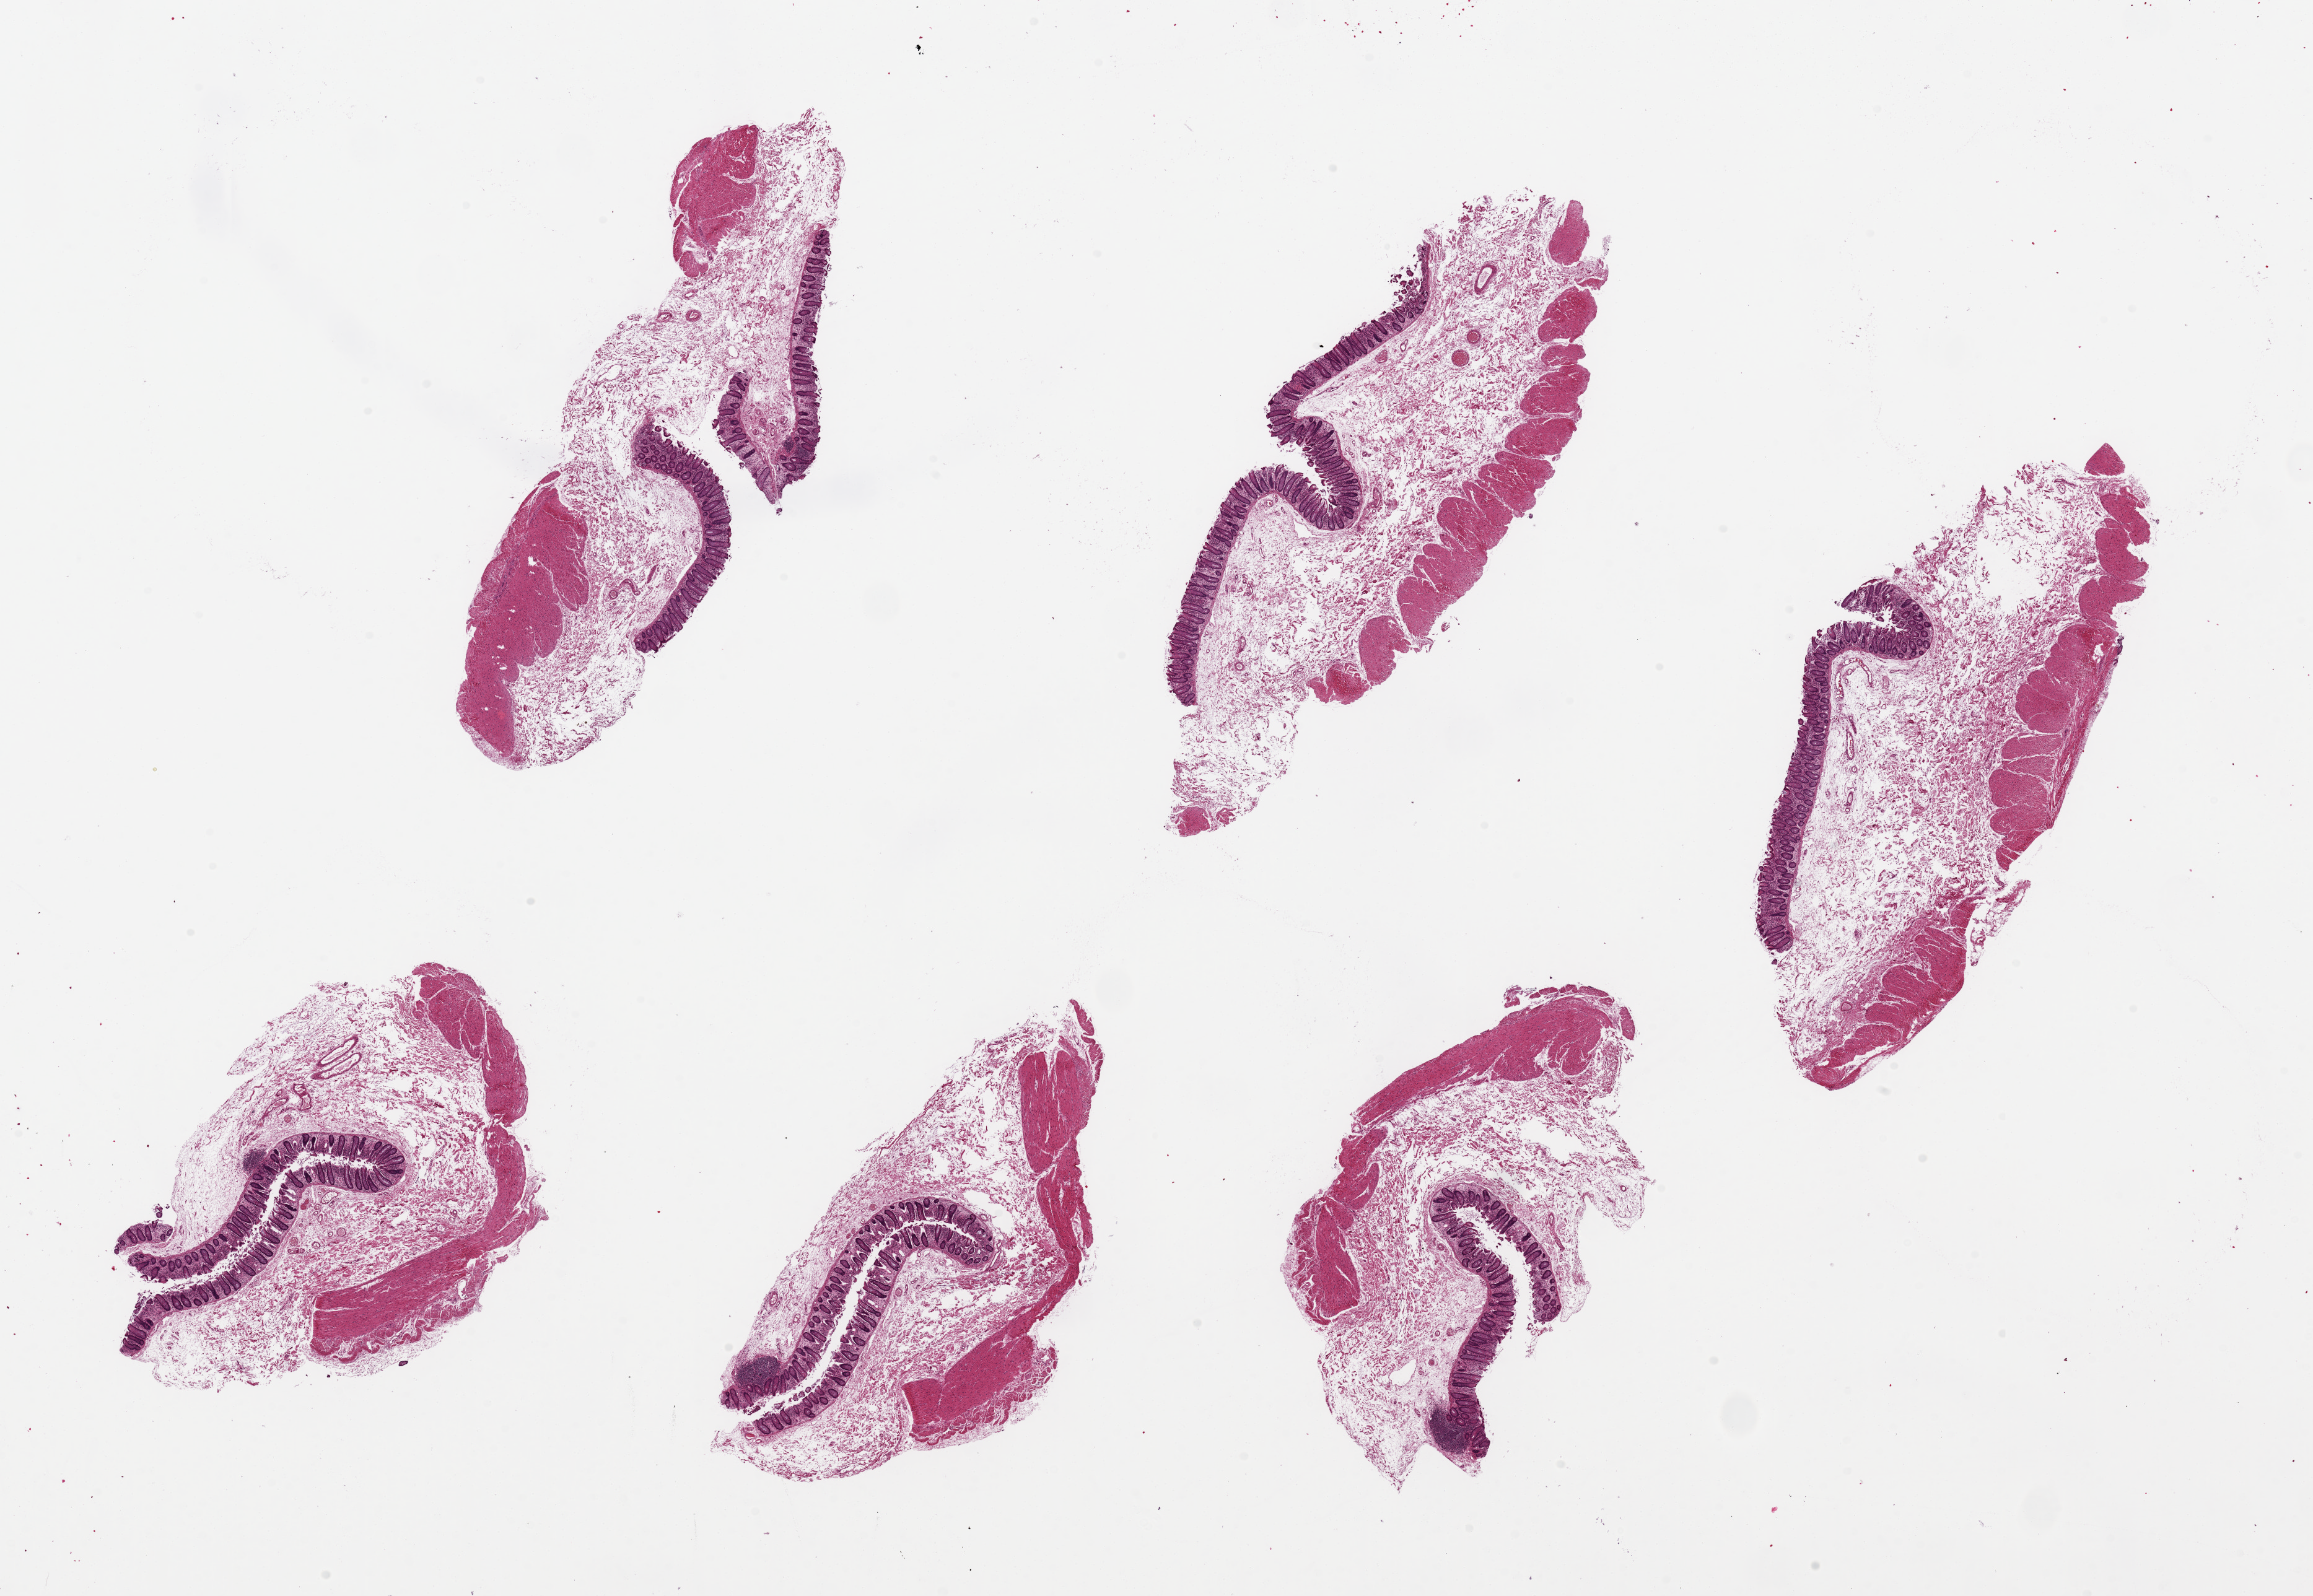
Digitized hematoxylin and eosin (H&E)-stained section, low-resolution overview of the scanned area, about 29.5 x 20.4 mm (from a 20x scan). PAXgene-fixed paraffin-embedded (PFPE) section. Target tissue: transverse colon. Donor tissue sample. Donor: female.
- review note (as recorded): 6 pieces `9x3mm, partially detached mucosa, `10% of thickness